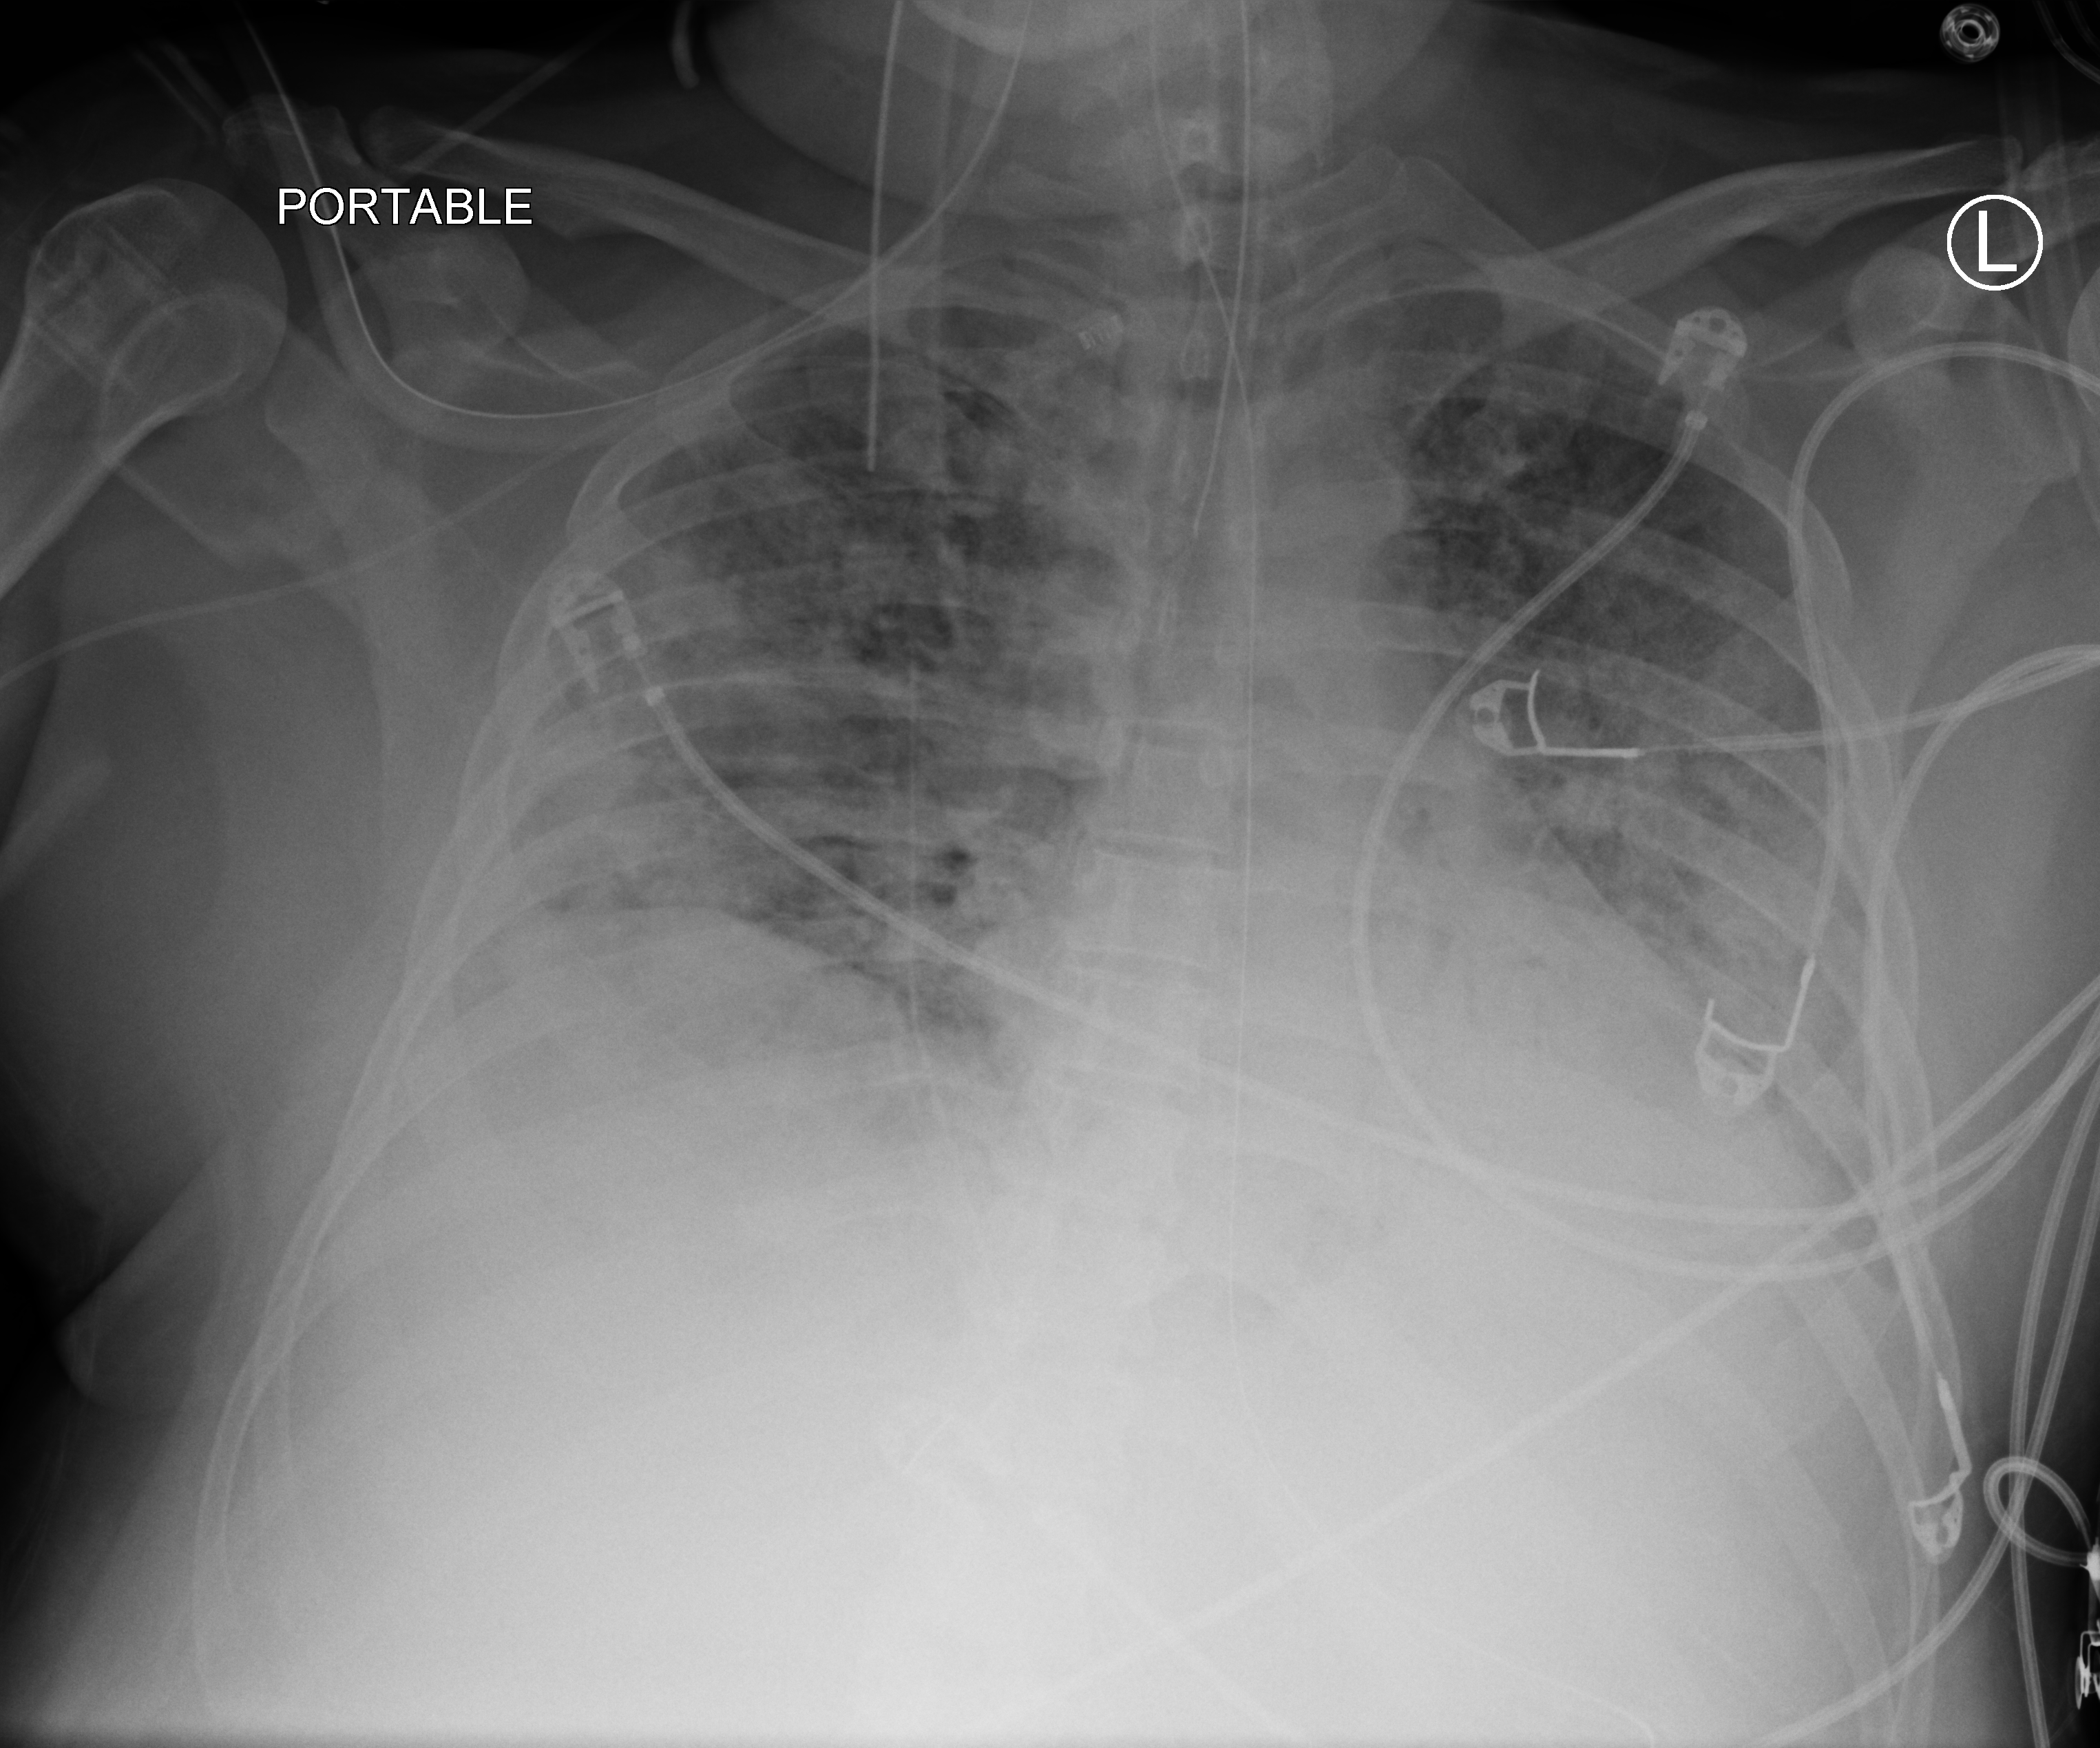
Chest X-ray (portable); anteroposterior (AP) projection. Patient hospitalised with COVID-19; male, aged 18–59 years.
Admission-level facts for this patient (not findings on this image; timing relative to this image not recorded):
- hypertension (admission record): no